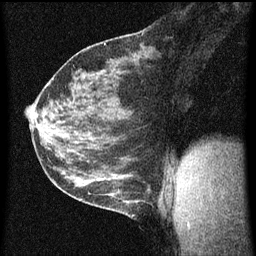
Breast MRI (dynamic contrast-enhanced), one sagittal slice. Position 31 of 60 along the scan axis. Dynamic contrast-enhanced series, image 2 of 3 at this slice position (ordered by acquisition). 1.5 T. TE 4.2 ms, TR 8 ms. 2 mm slice thickness. 256 × 256 image matrix. Female patient, age 35 years.
Annotated regions visible in this slice (semi-automatic segmentation, software-assisted and operator-edited):
- analysis volume of interest (the breast-tissue region the enhancement analysis was run in; not a lesion): bounding box (x1, y1, x2, y2) in pixels: (106, 182, 149, 219)
- tumour enhancement mask (voxels above the 70 % enhancement threshold inside the analysis volume of interest): (116, 190, 125, 203)